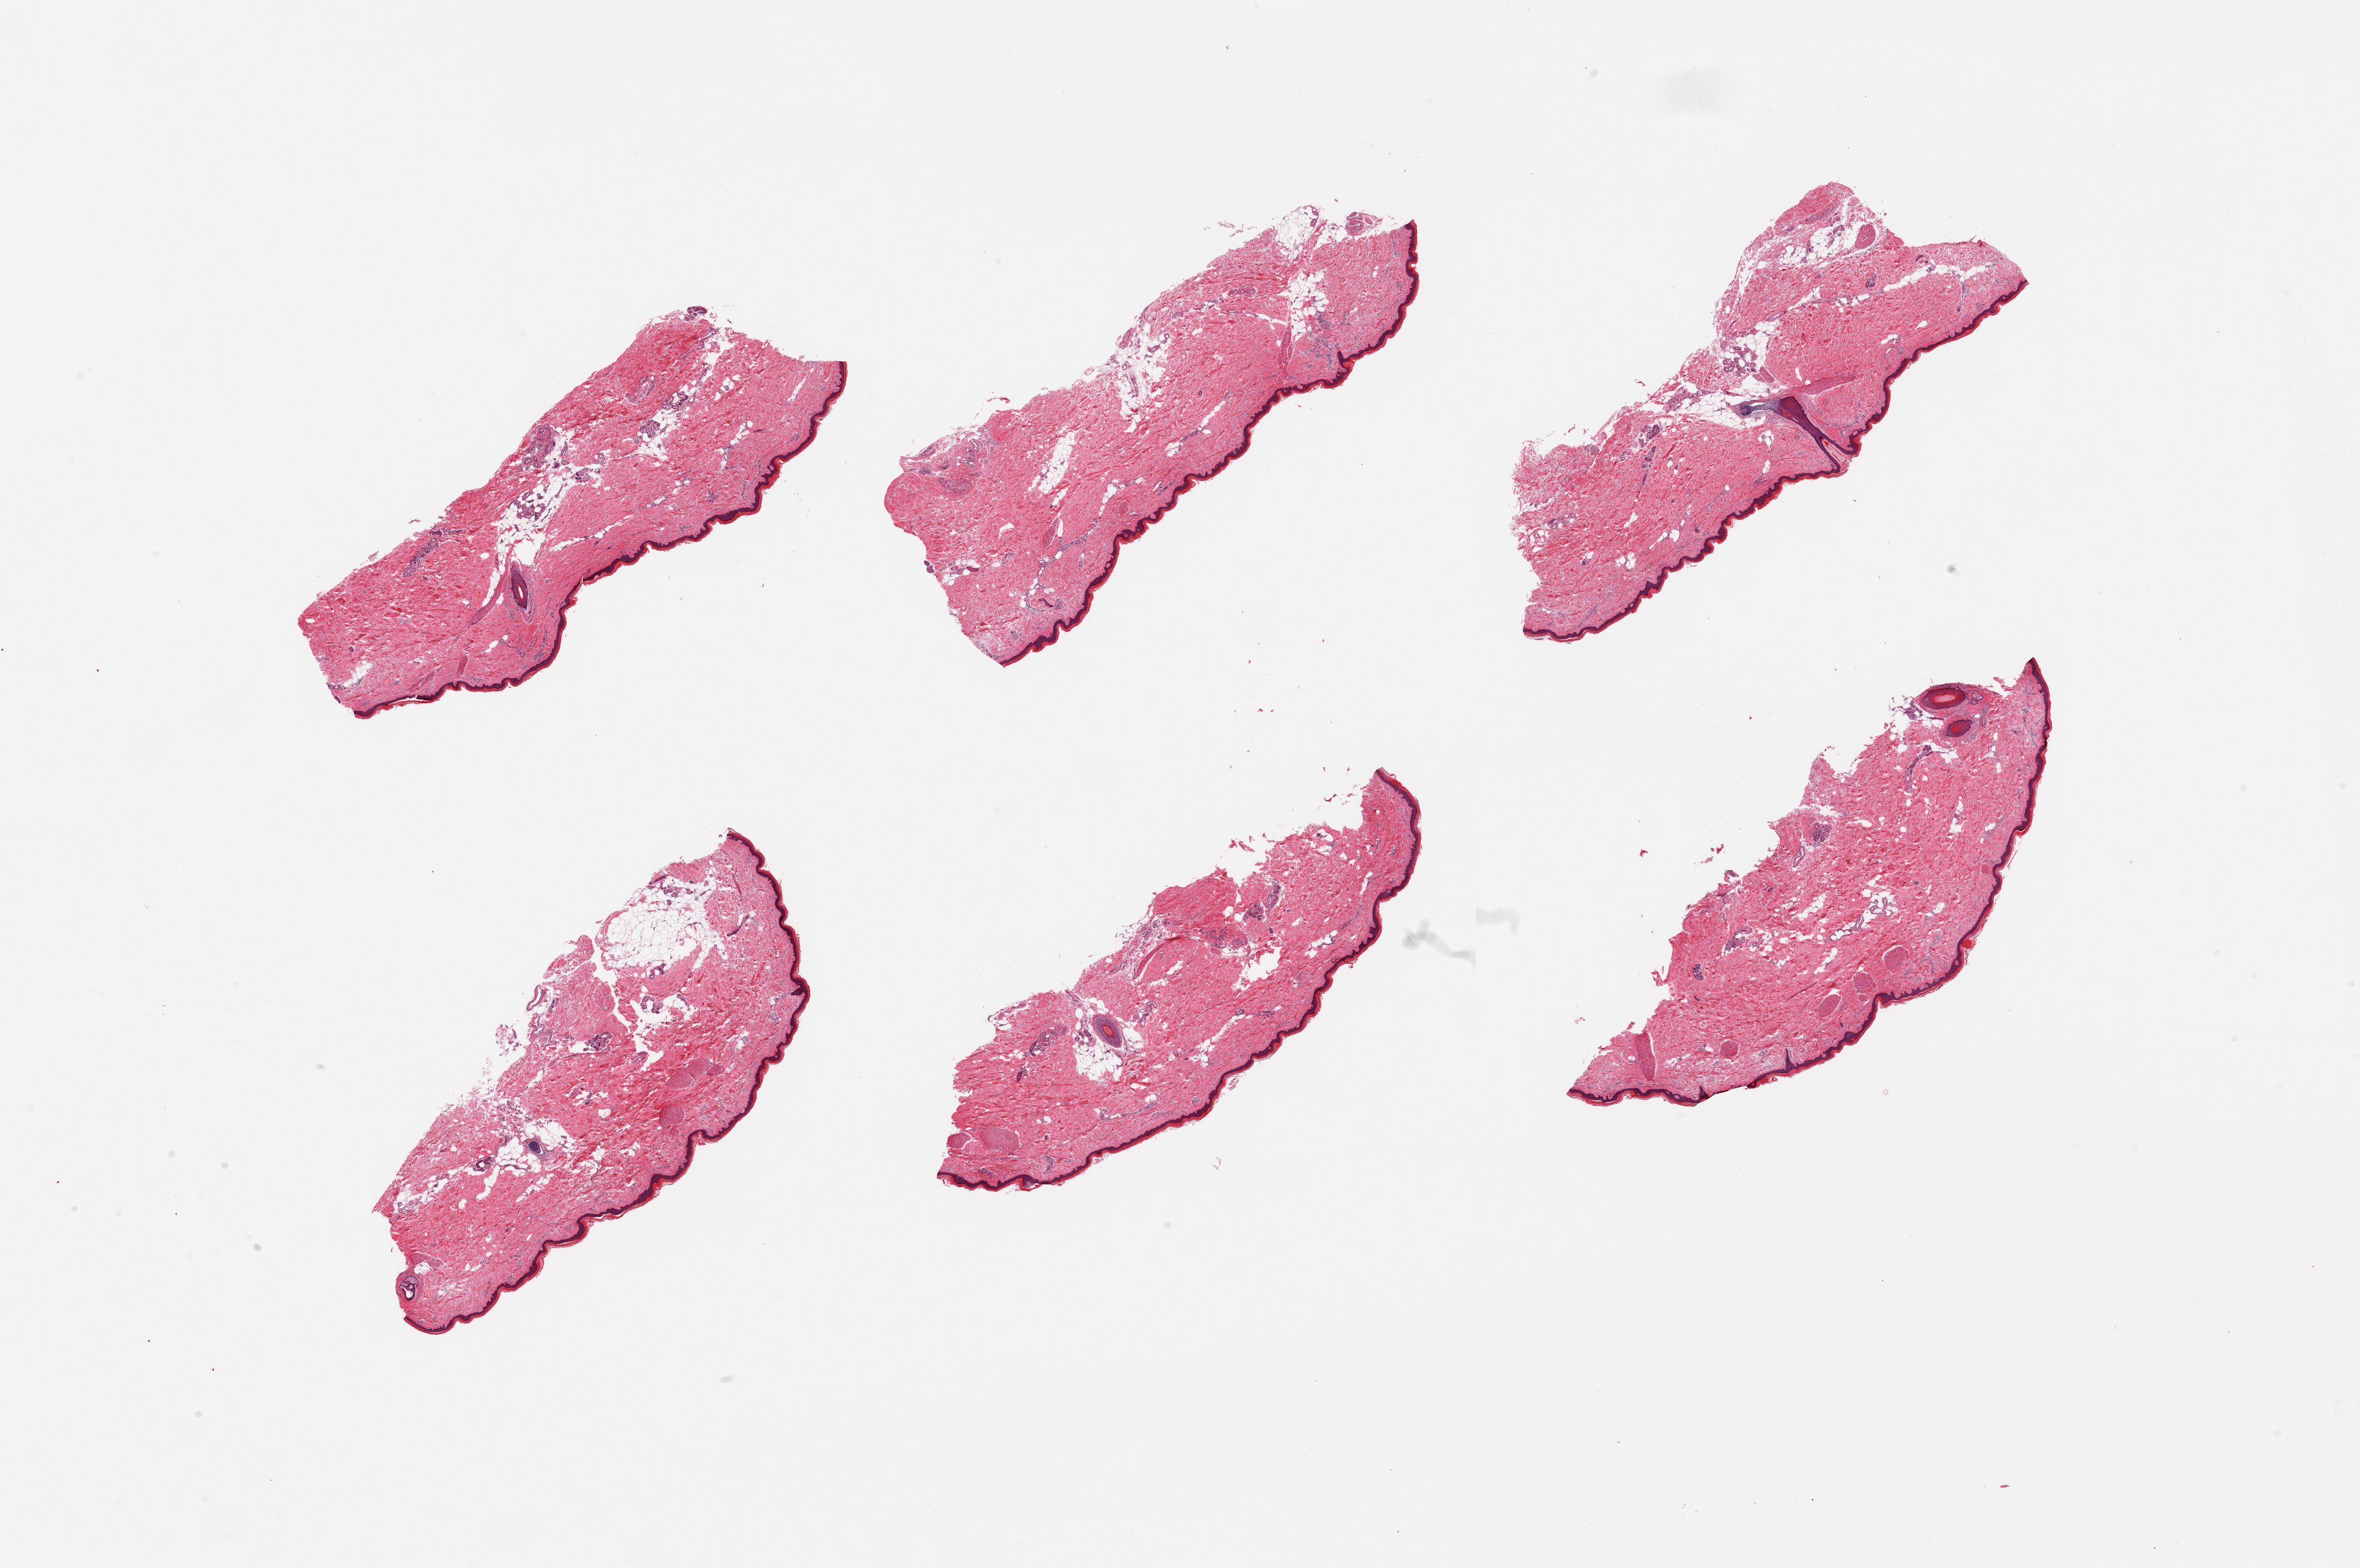
Hematoxylin and eosin (H&E) whole-slide image, brightfield — low-resolution overview of the scanned area, about 31.5 x 20.9 mm; PAXgene-fixed paraffin-embedded (PFPE) section; sampled site (target tissue): skin of lower leg; donor tissue sample.
Review note (as recorded): 6 pieces, minimal adherent fat, squamous epithelium is ~60 microns.